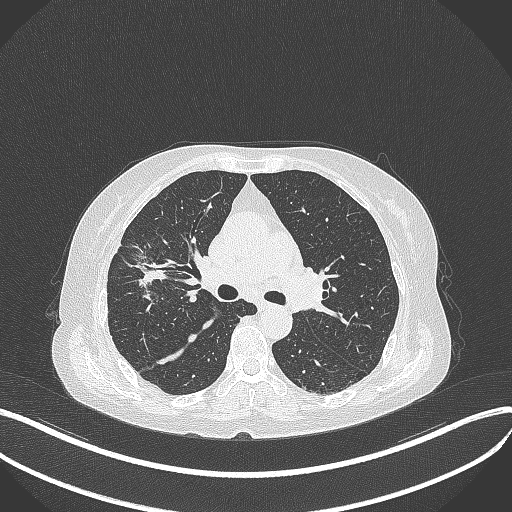
Chest CT, one axial slice. Lung window (W 1500 / L -600 HU). 512 × 512 image matrix, field of view 400 × 400 mm. Patient: female, 69 years. Case-level facts recorded for this patient, not image findings: clinical TNM (as recorded): T1b N3 M0.
Annotated regions visible in this slice (rectangle marked by the reading radiologist):
- lung tumour (recorded histology: small cell carcinoma): bounding box <122,252,174,292> (left, top, right, bottom; pixels)